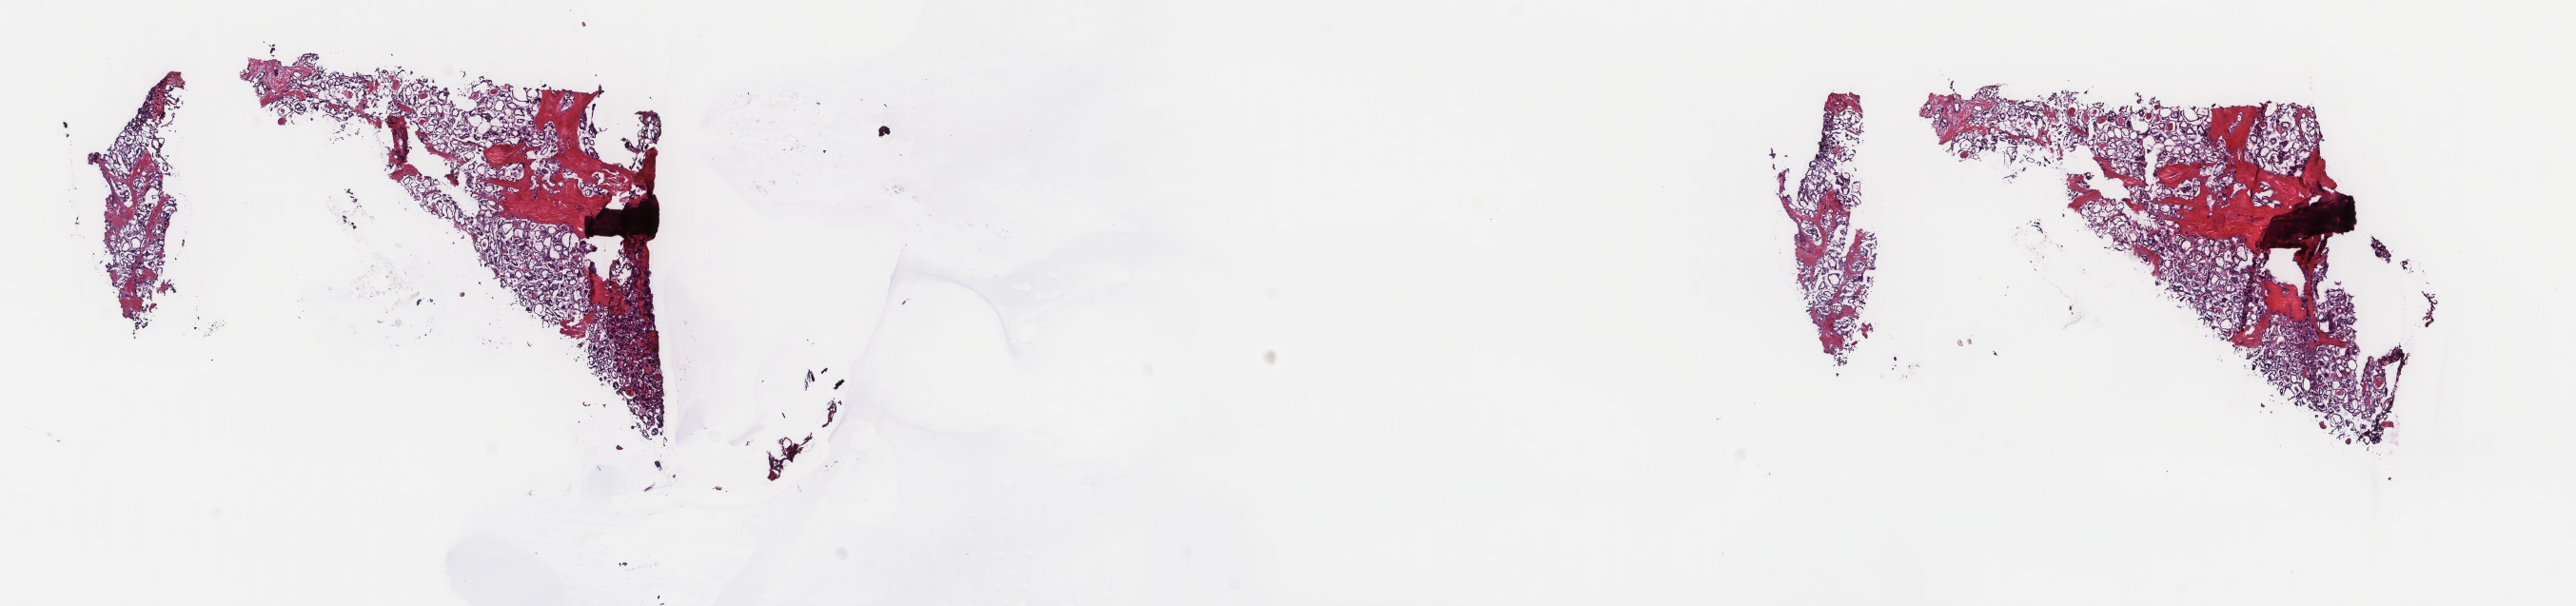
Digitized Hematoxylin and eosin (H&E) stained tissue section (whole slide) — shown as a low-resolution overview of the whole scanned area (about 21.5 x 5.1 mm, from a 40x scan). Frozen section from the top of the tissue portion. Sample: primary tumour, thyroid. Patient: female, age at initial diagnosis 43 years. Composition of this section per pathologist review: tumour cells 70%, tumour nuclei 100%, normal cells 0%, stromal cells 30%, necrosis 0%. Inflammatory infiltration, as recorded: lymphocyte infiltration 0%, monocyte infiltration 0%, neutrophil infiltration 0%.
- AJCC pathologic stage: I
- diagnosis: Papillary carcinoma, follicular variant
- laterality: left
- TNM: T3 N1b MX